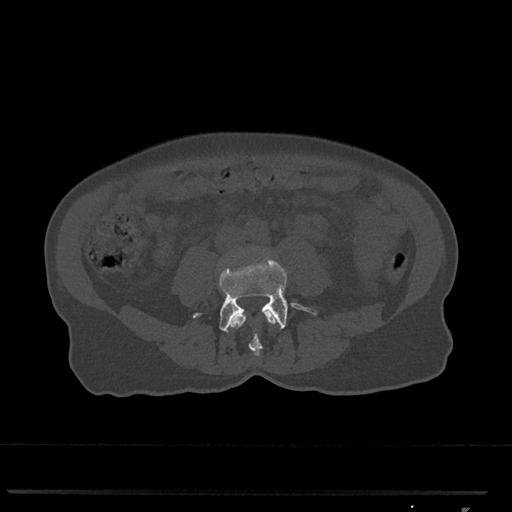
CT including the spine, one axial slice; position 229 of 793 along the scan axis; bone window (W 1800 / L 400 HU); 0.5 mm slice thickness; 512 × 512 image matrix, field of view 380 × 380 mm. Female patient, age 62 years. Case-level facts recorded for this patient, not image findings: primary cancer: renal.
Outlined on this slice (semi-automatically segmented with operator editing):
- L3 vertebra: bounding box (x1, y1, x2, y2) in pixels: (230, 311, 276, 356)
- L4 vertebra: (193, 258, 317, 333)